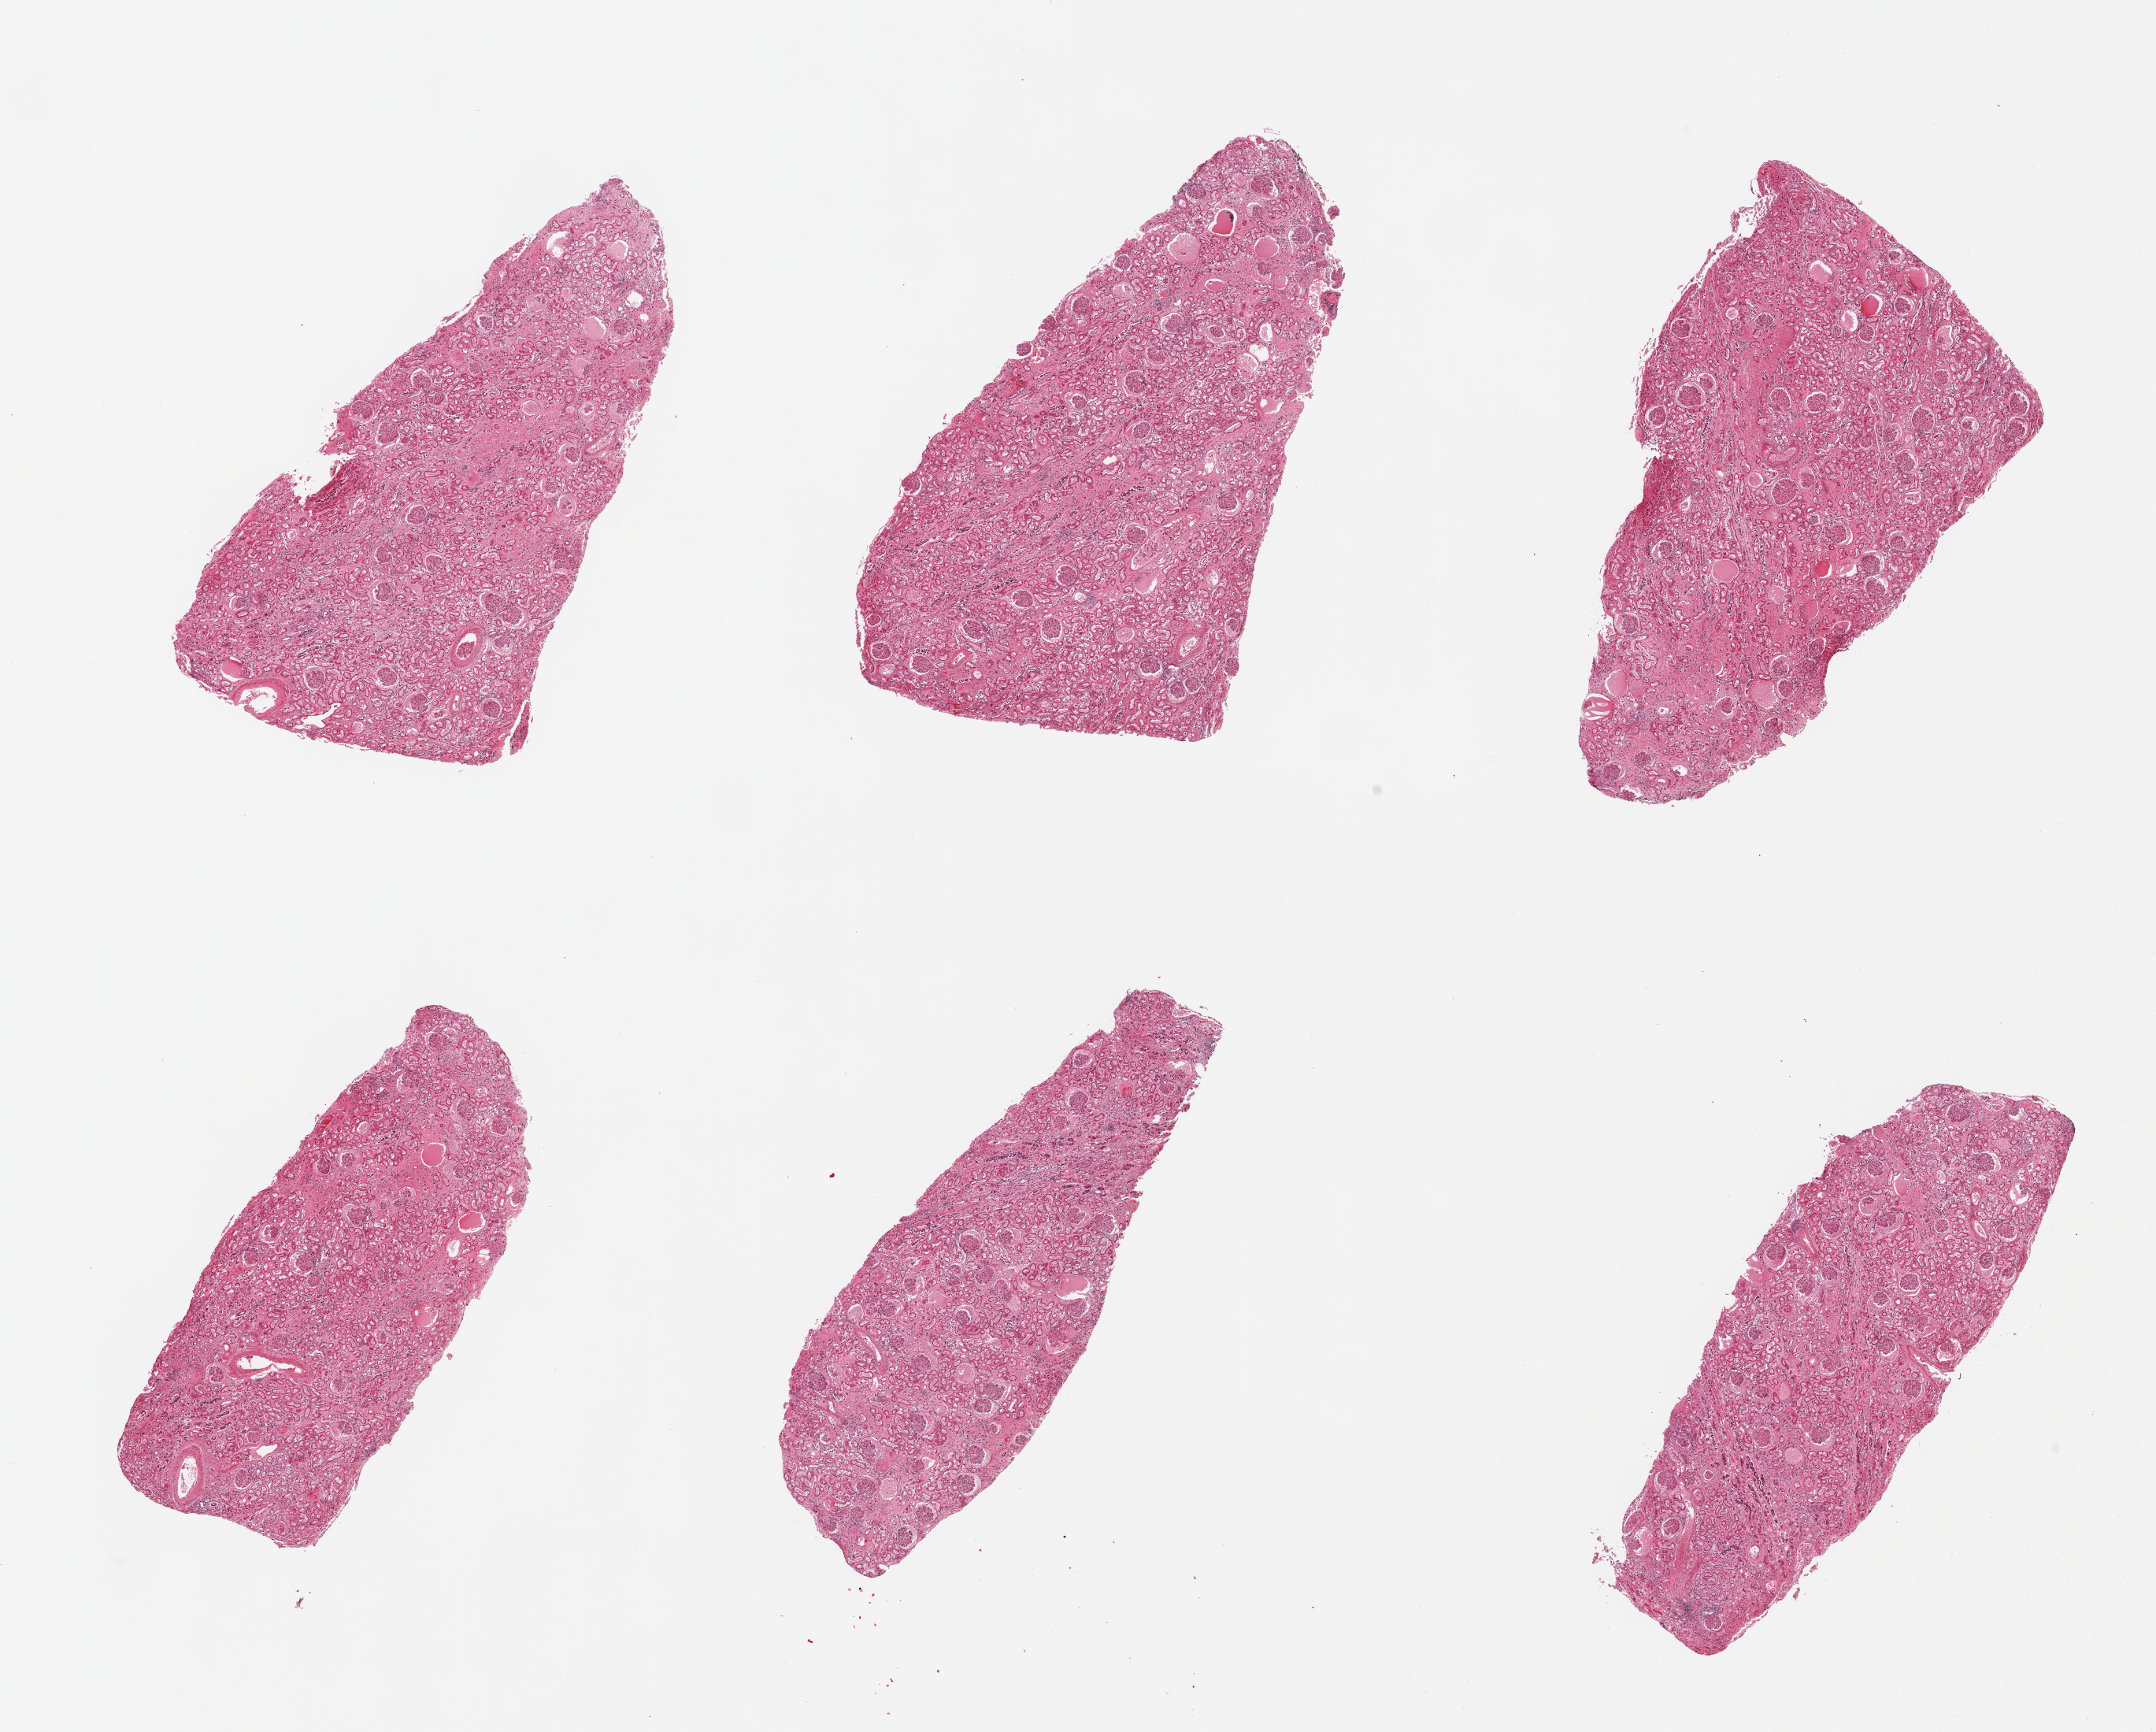
Whole-slide image, H&E stain, shown as a low-resolution overview of the whole scanned area (about 21.7 x 17.4 mm), PAXgene-fixed paraffin-embedded (PFPE) section, sampled site (target tissue): renal cortex, tissue donor sample. Donor: male.
Review note (as recorded): 6 pieces; 10% interstitial scarring.